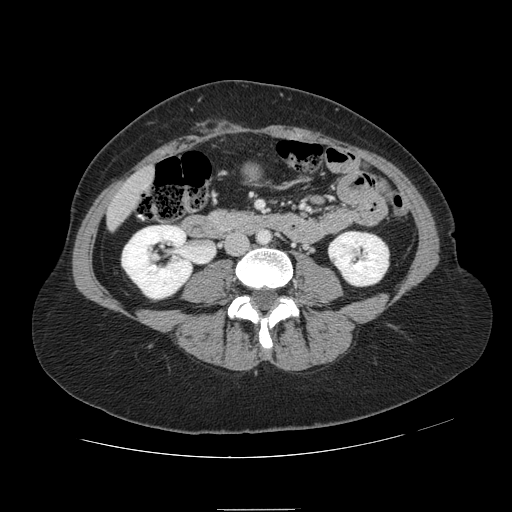
Contrast-enhanced abdominal CT, one axial slice; slice 6 of 121 in the series (ordered by position); intravenous contrast given; soft-tissue window (W 400 / L 40 HU); 2.5 mm slice thickness; 512 × 512 image matrix, field of view 400 × 400 mm. Female patient, age 52 years. From the clinical record (not read from this slice): diagnosis: colorectal cancer liver metastases, imaged before liver resection; multiple liver metastases: yes; largest metastasis: 6.3 cm; disease in both lobes: no.
Structures marked on this image (expert manual segmentation):
- liver: box from (x=109, y=169) to (x=154, y=227) px